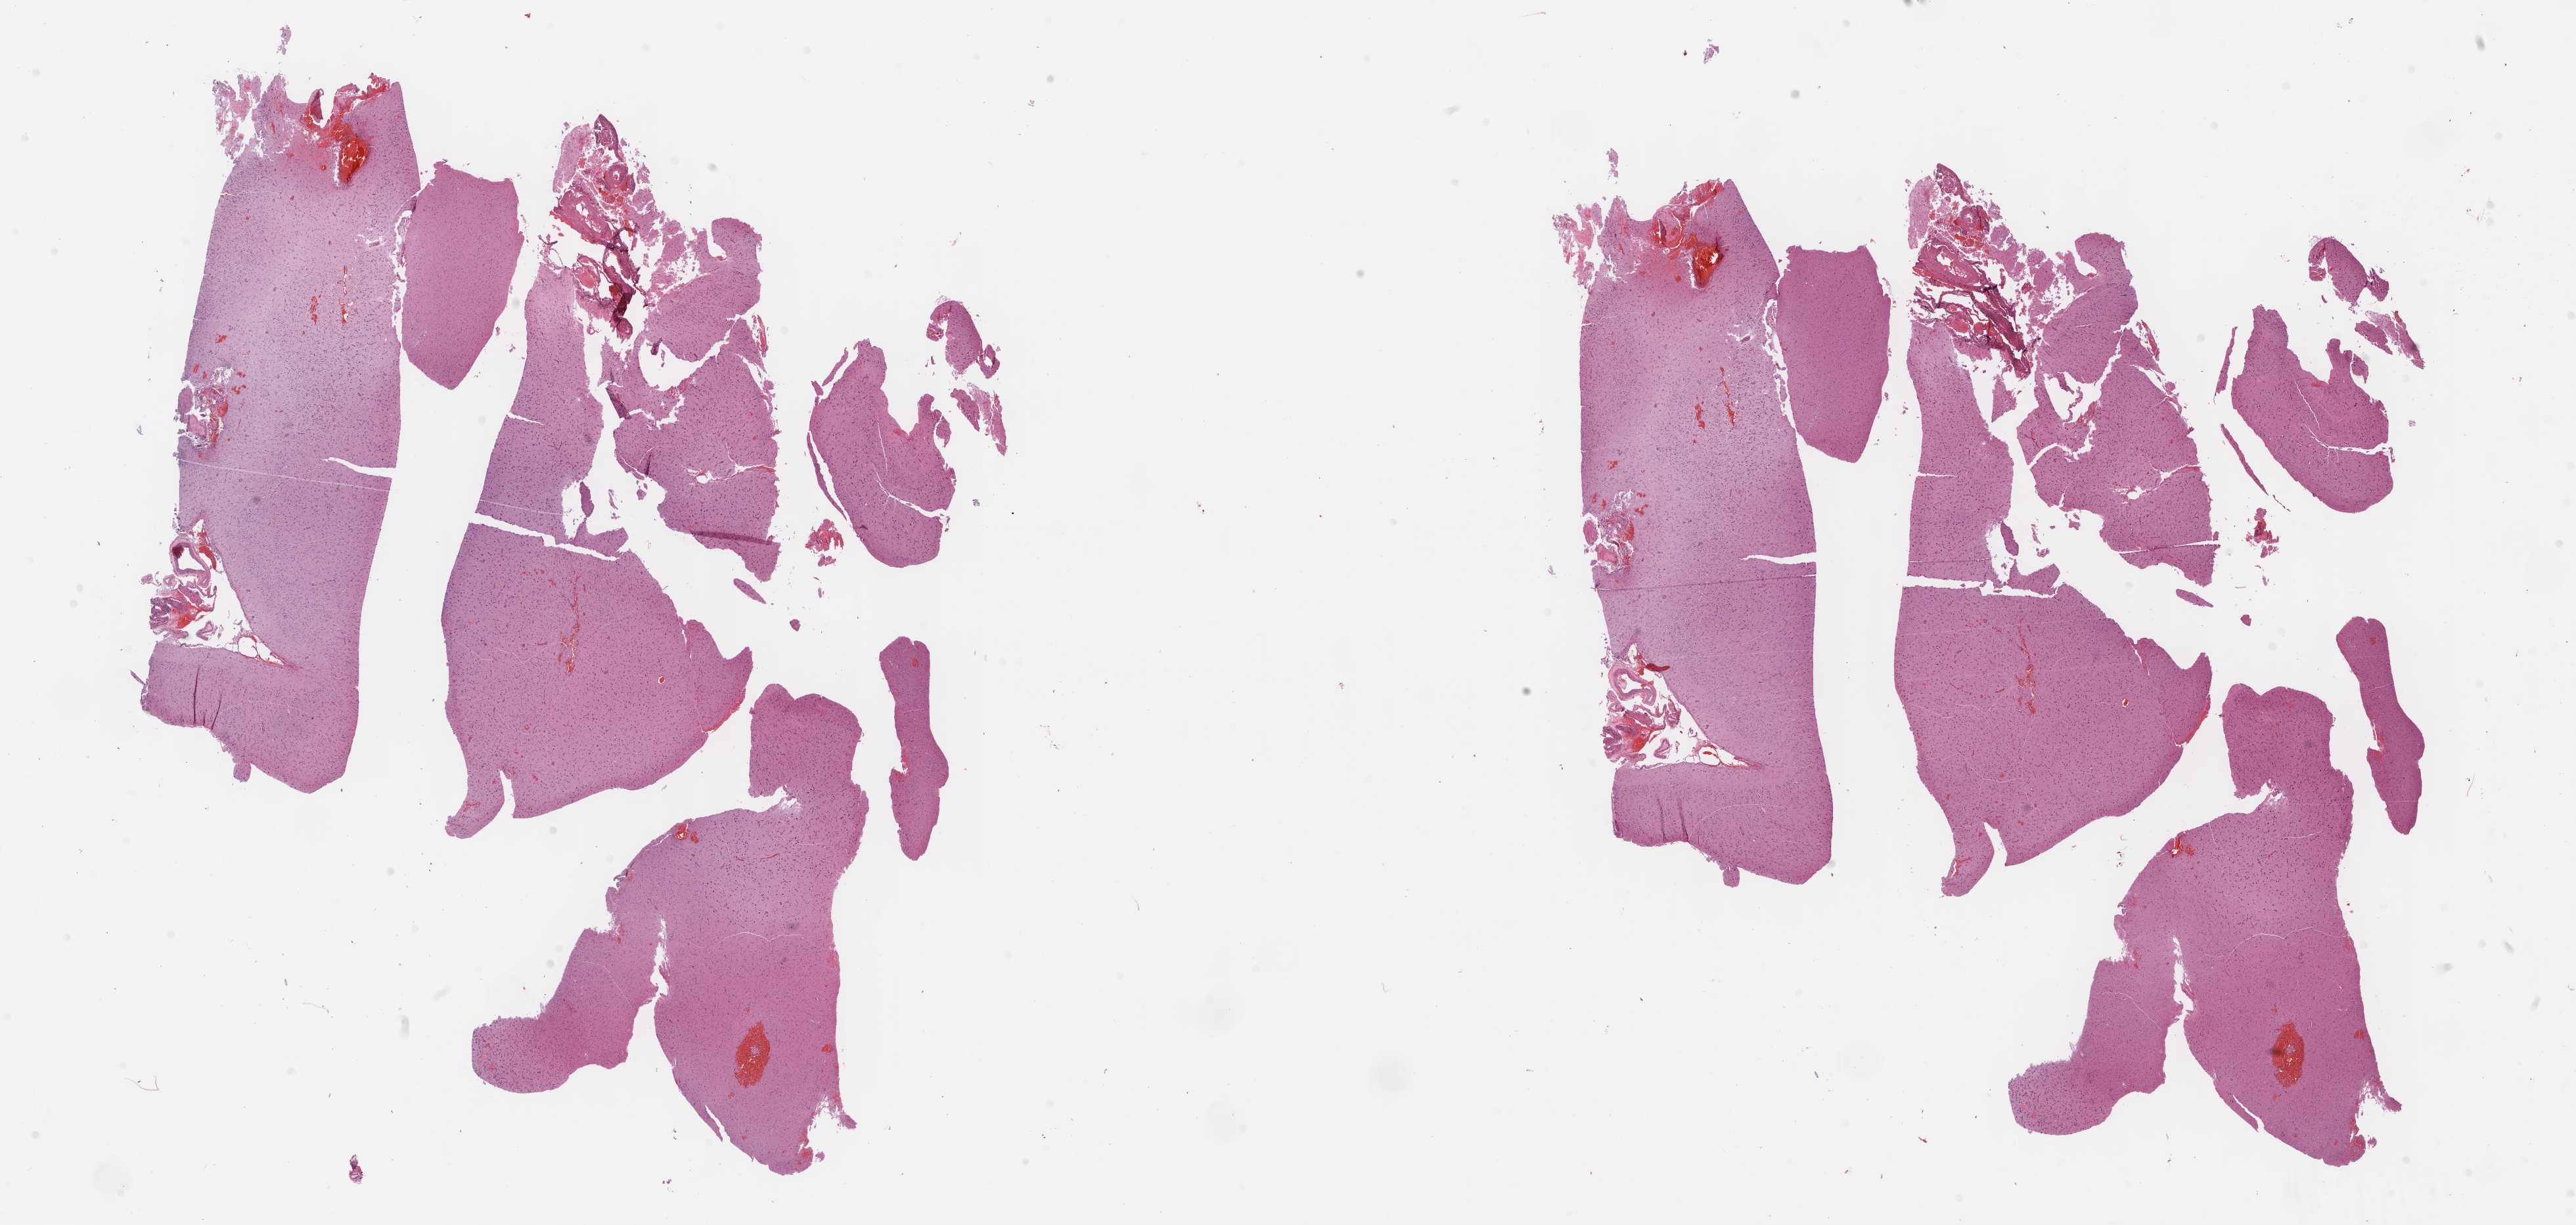
H&E-stained whole-slide image — shown as a low-resolution overview of the whole scanned area (about 31.7 x 15.1 mm), FFPE section, brain, primary tumour sample. Female, age 61 years at initial diagnosis.
Pathologic diagnosis: Astrocytoma, anaplastic (cerebrum).